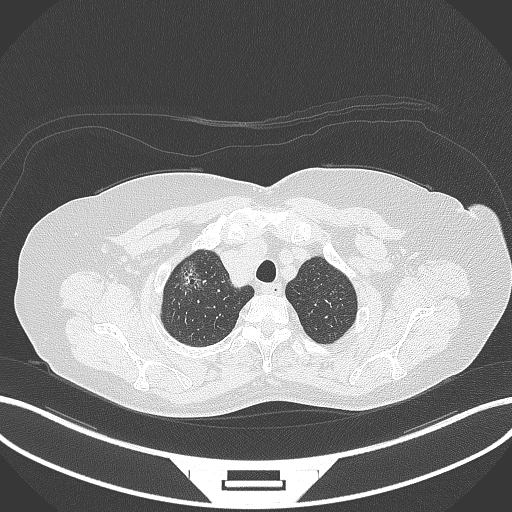
Chest CT, one axial slice. Slice 307 of 365 in the series (ordered by position). Reconstruction kernel B70f. 120 kVp. Lung window (W 1500 / L -600 HU). 1 mm slice thickness. 512 × 512 image matrix. Female patient, age 62 years. From the clinical record (not read from this slice): clinical TNM (as recorded): T1c N0 M0.
Annotated regions visible in this slice (bounding box drawn by a radiologist):
- lung tumour (recorded histology: adenocarcinoma): bounding box [x1, y1, x2, y2] px = [174, 257, 209, 296]